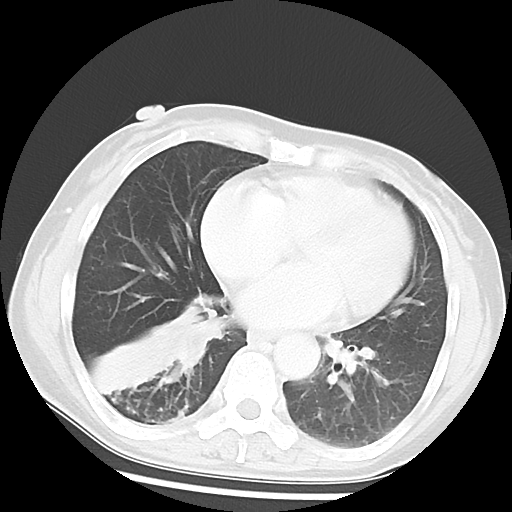
Chest CT, one axial slice; slice 23 of 52 in the series (ordered by position); lung window (W 1500 / L -600 HU); 5 mm slice thickness; 512 × 512 image matrix, field of view 297 × 297 mm. Patient: female, 54 years. Case-level facts recorded for this patient, not image findings: clinical TNM (as recorded): T1c N0 M0; histopathological grade: G1-2.
Structures marked on this image (bounding box drawn by a radiologist):
- lung tumour (recorded histology: squamous cell carcinoma): bounding box <169,301,220,374> (left, top, right, bottom; pixels)